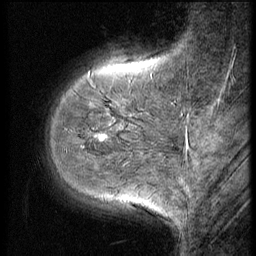
Breast MRI (dynamic contrast-enhanced), one sagittal slice. Position 13 of 56 along the scan axis. 3 images stored at this slice position (order not interpretable as contrast timing). 1.5 T. TE 4.2 ms, TR 9 ms. 2.5 mm slice thickness. 256 × 256 image matrix, field of view 180 × 180 mm. Female patient, age 49 years. From the clinical record (not read from this slice): setting: breast cancer imaged before/during neoadjuvant chemotherapy; receptor status: HER2-positive.
Annotated regions visible in this slice (semi-automatic segmentation, software-assisted and operator-edited):
- analysis volume of interest (the breast-tissue region the enhancement analysis was run in; not a lesion): bounding box <41,74,148,198> (left, top, right, bottom; pixels)
- tumour enhancement mask (voxels above the 140 % enhancement threshold inside the analysis volume of interest): <96,135,105,142>